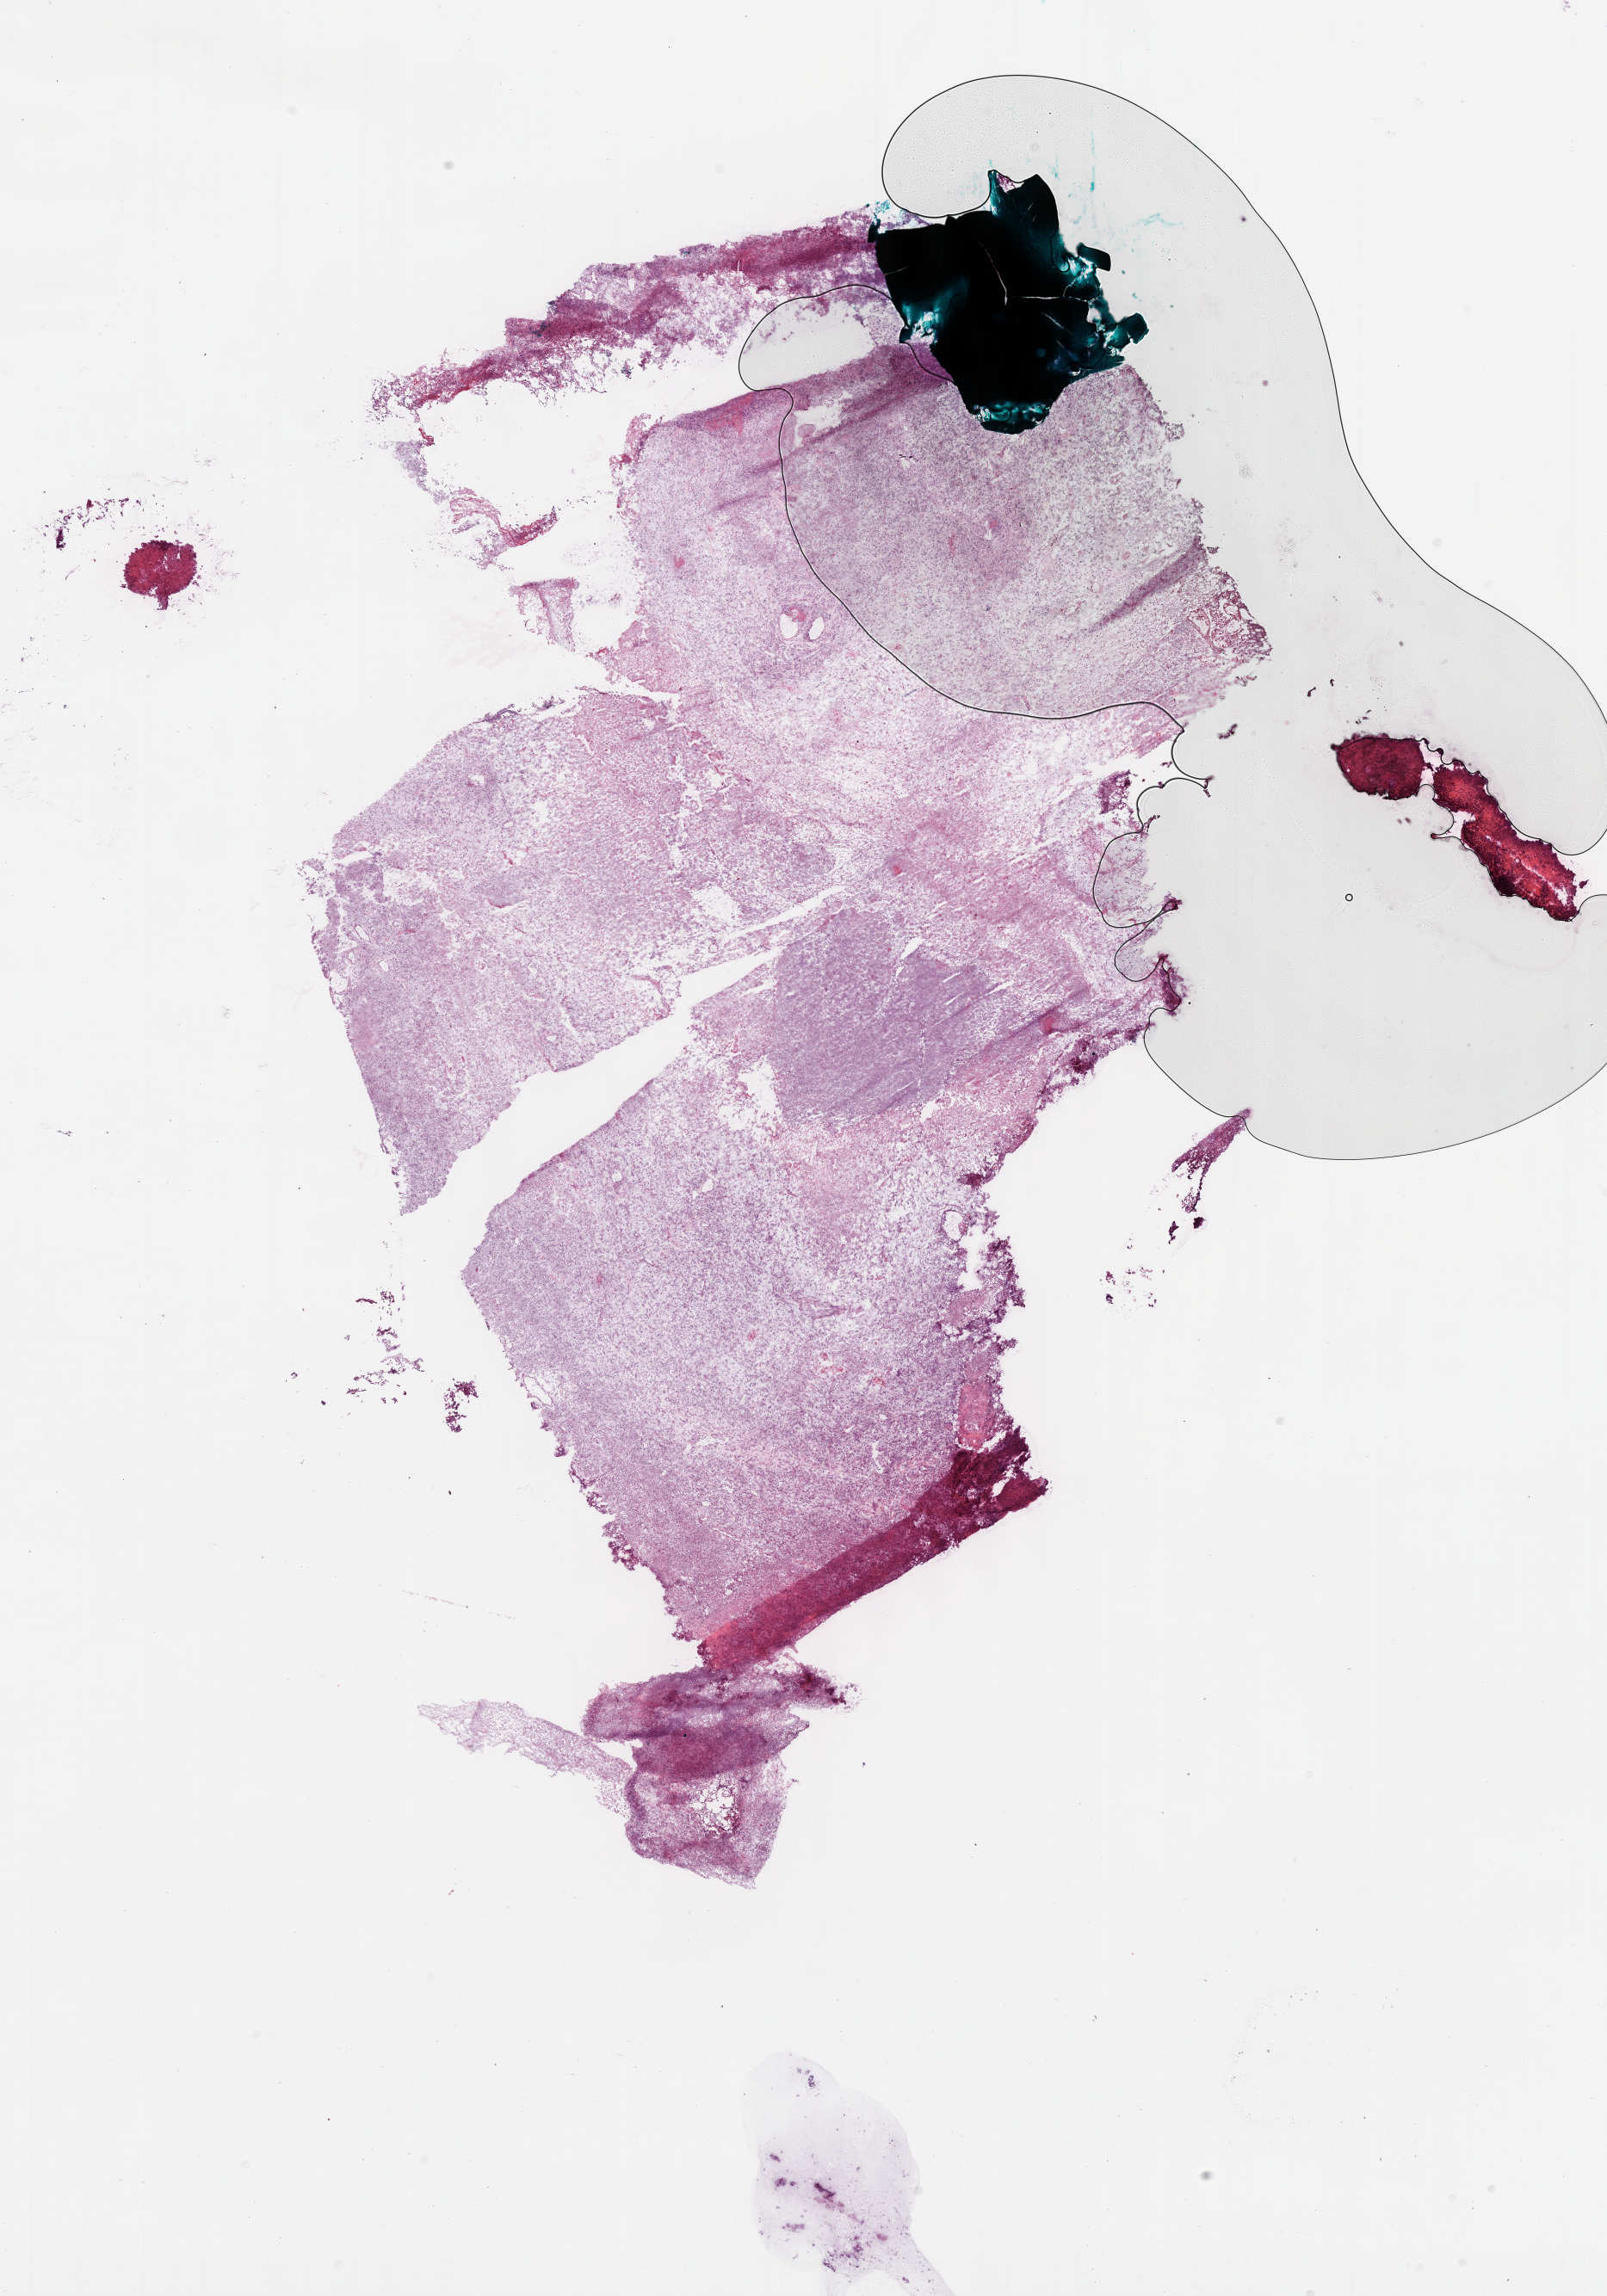
Digitized H&E tissue section (whole slide) — whole scanned area (about 15.1 x 21.6 mm) shown as a low-resolution overview, frozen section, sample: primary tumour, brain. Male patient; age at initial diagnosis 50 years. Pathologist review of this section (percent, as recorded): tumour cells 60%, tumour nuclei 95%, normal cells 0%, stromal cells 0%, necrosis 40%.
• diagnosis: Glioblastoma